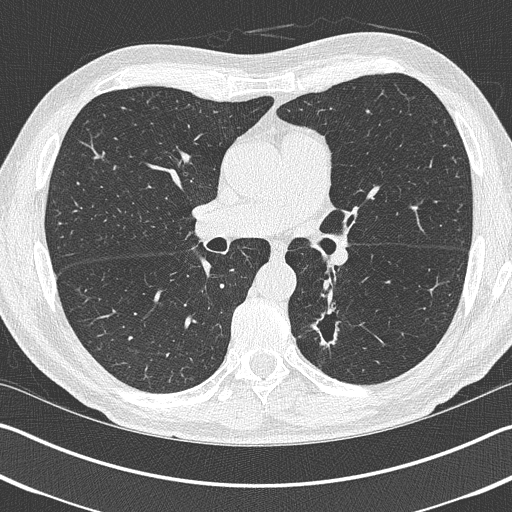
Low-dose screening chest CT, one axial slice; position 233 of 402 along the scan axis; lung window (W 1500 / L -600 HU); 512 × 512 image matrix, field of view 340 × 340 mm.
Outlined on this slice (expert manual segmentation):
- lesion 1 (tumor, lower lobe of left lung): bounding box <311,305,339,347> (left, top, right, bottom; pixels)